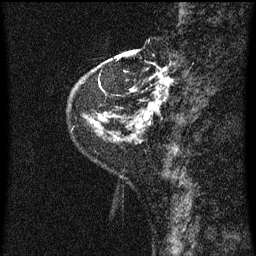
Breast MRI (dynamic contrast-enhanced), one sagittal slice. Position 11 of 60 along the scan axis. Dynamic contrast-enhanced series, image 2 of 3 at this slice position (ordered by acquisition). 1.5 T. TE 4.2 ms, TR 8 ms. 256 × 256 image matrix, field of view 180 × 180 mm. Female patient, age 48 years.
Annotated regions visible in this slice (semi-automatically segmented with operator editing):
- analysis volume of interest (the breast-tissue region the enhancement analysis was run in; not a lesion): bounding box <128,54,174,125> (left, top, right, bottom; pixels)
- tumour enhancement mask (voxels above the 70 % enhancement threshold inside the analysis volume of interest): <129,64,172,125>